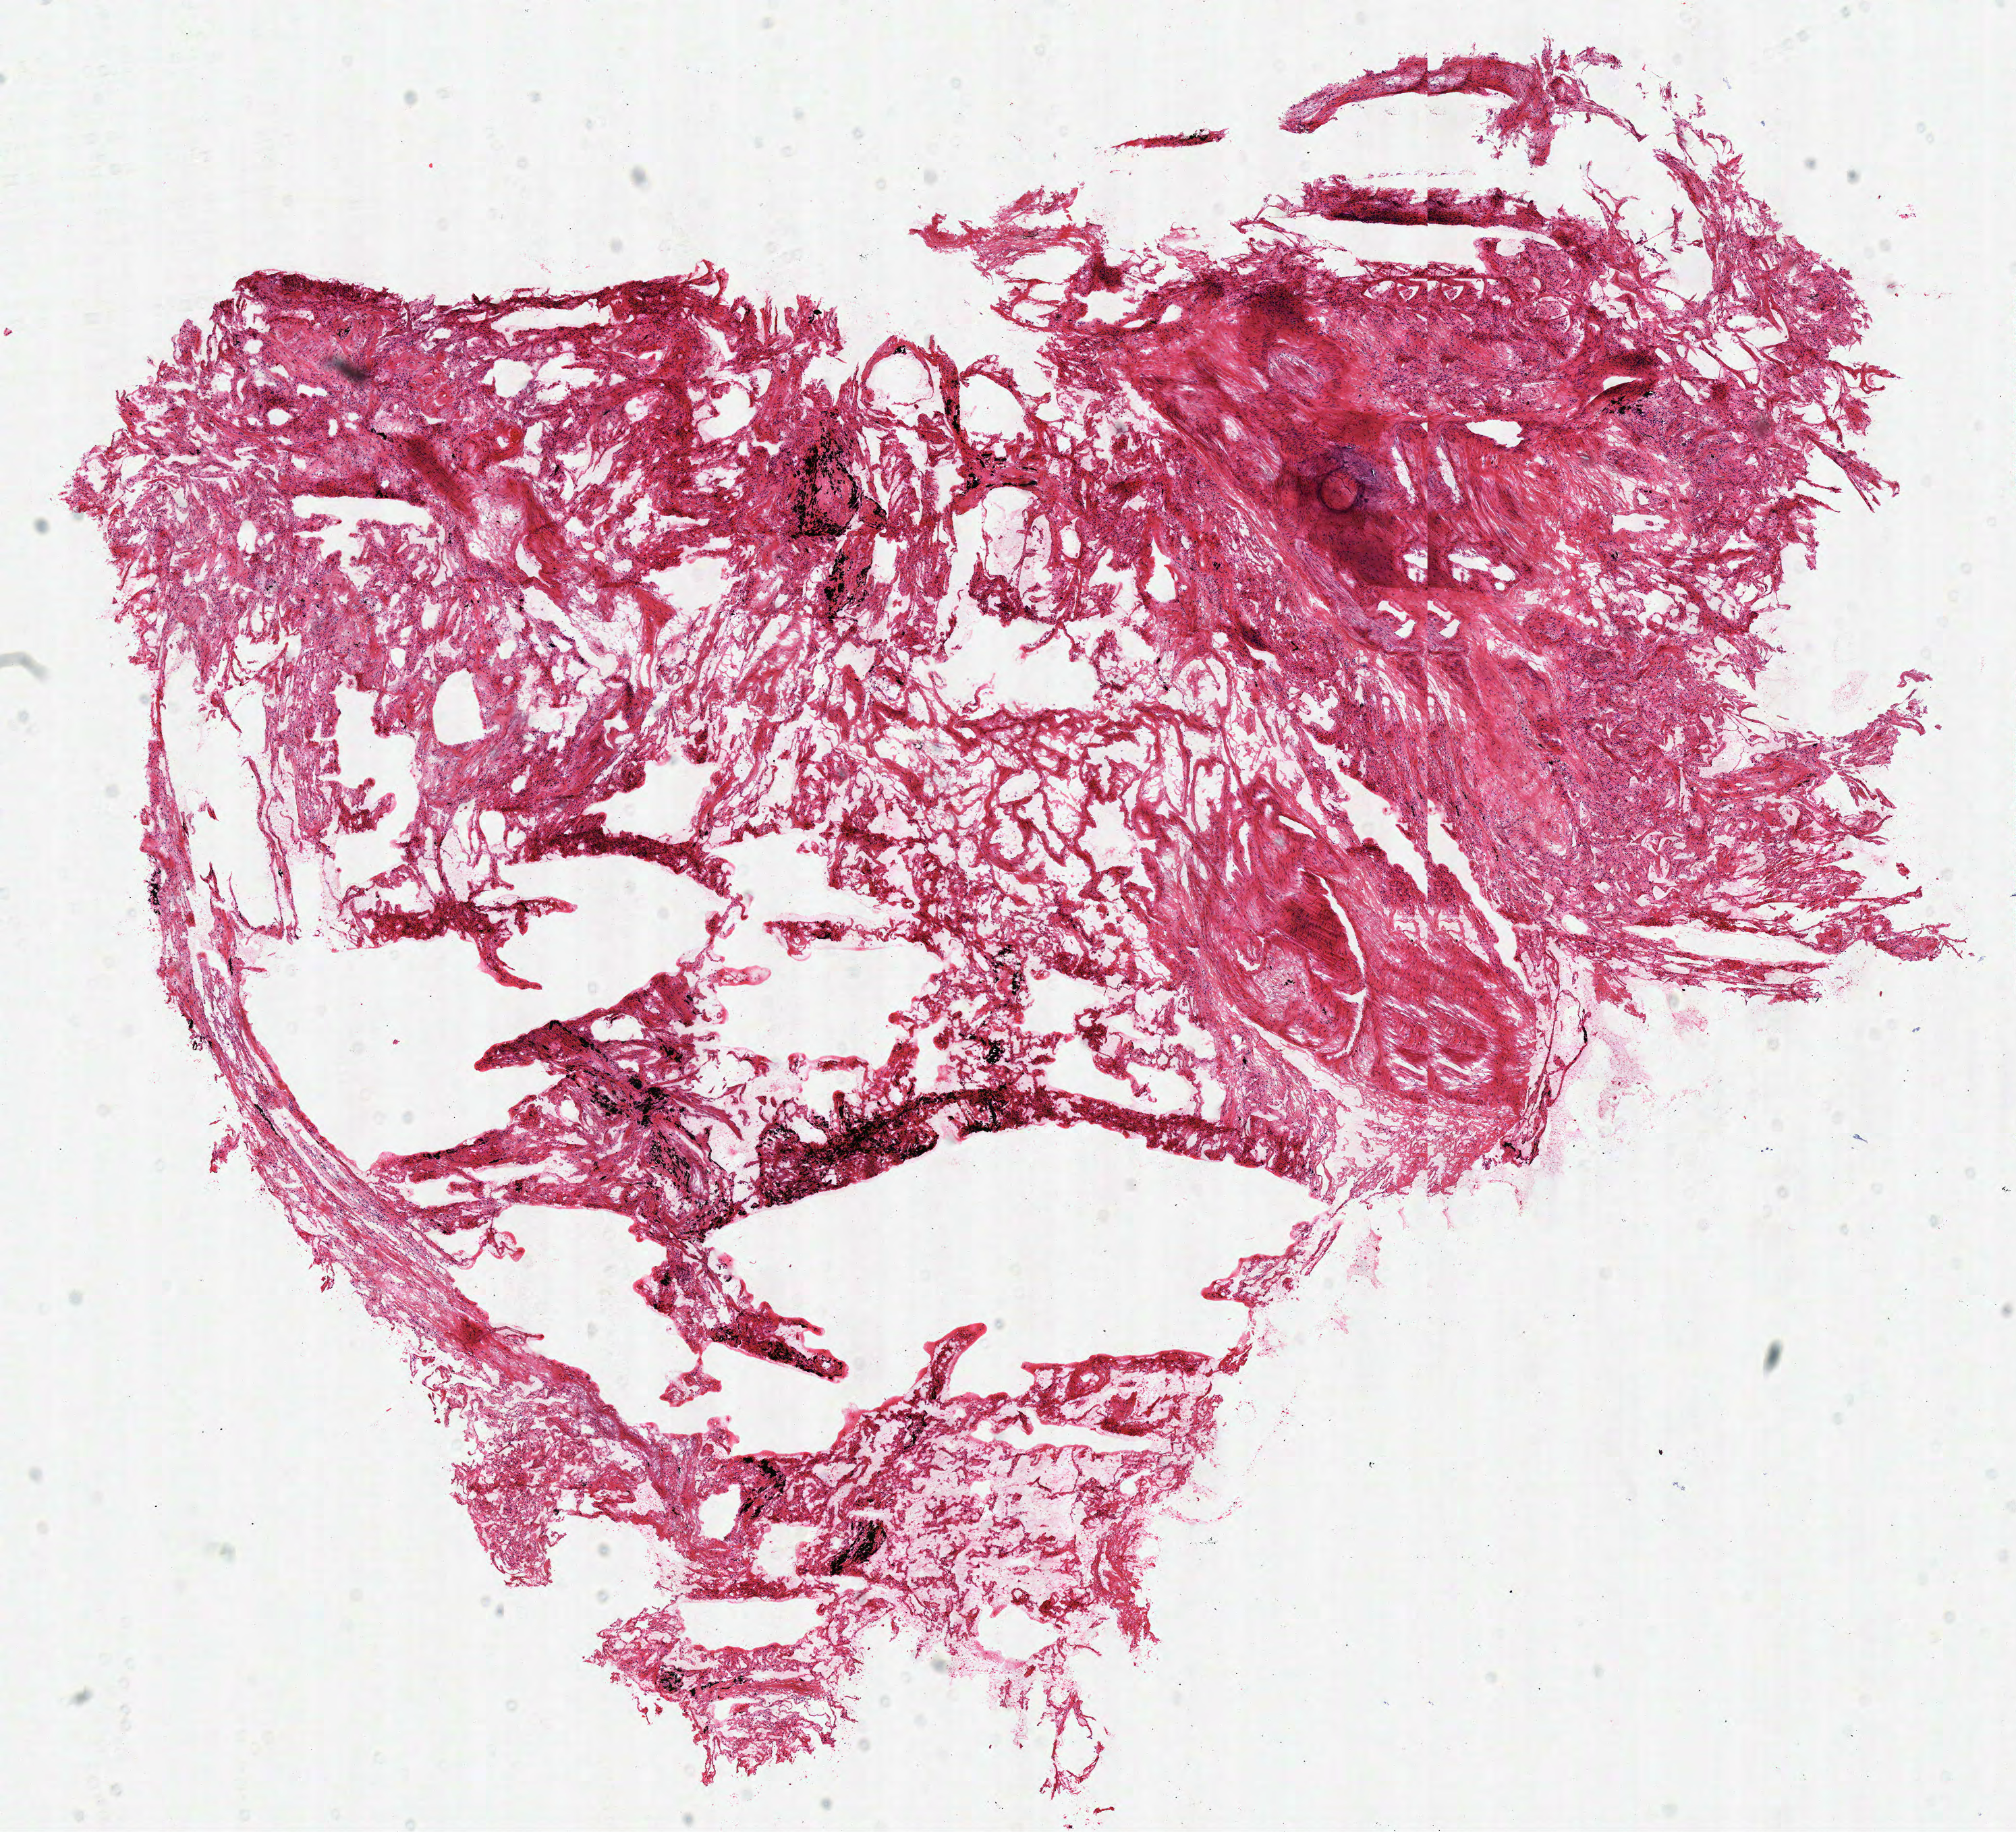
Digitized H&E-stained tissue section (whole slide) — shown as a low-resolution overview of the whole scanned area (about 11.7 x 10.7 mm, from a 40x scan). Frozen section. Sample: solid tissue normal (non-tumour tissue), lung. Patient: female, age at initial diagnosis 75 years.
This section: solid tissue normal (non-tumour) sample from the same patient. Patient diagnosis: Adenocarcinoma, NOS (upper lobe, lung).